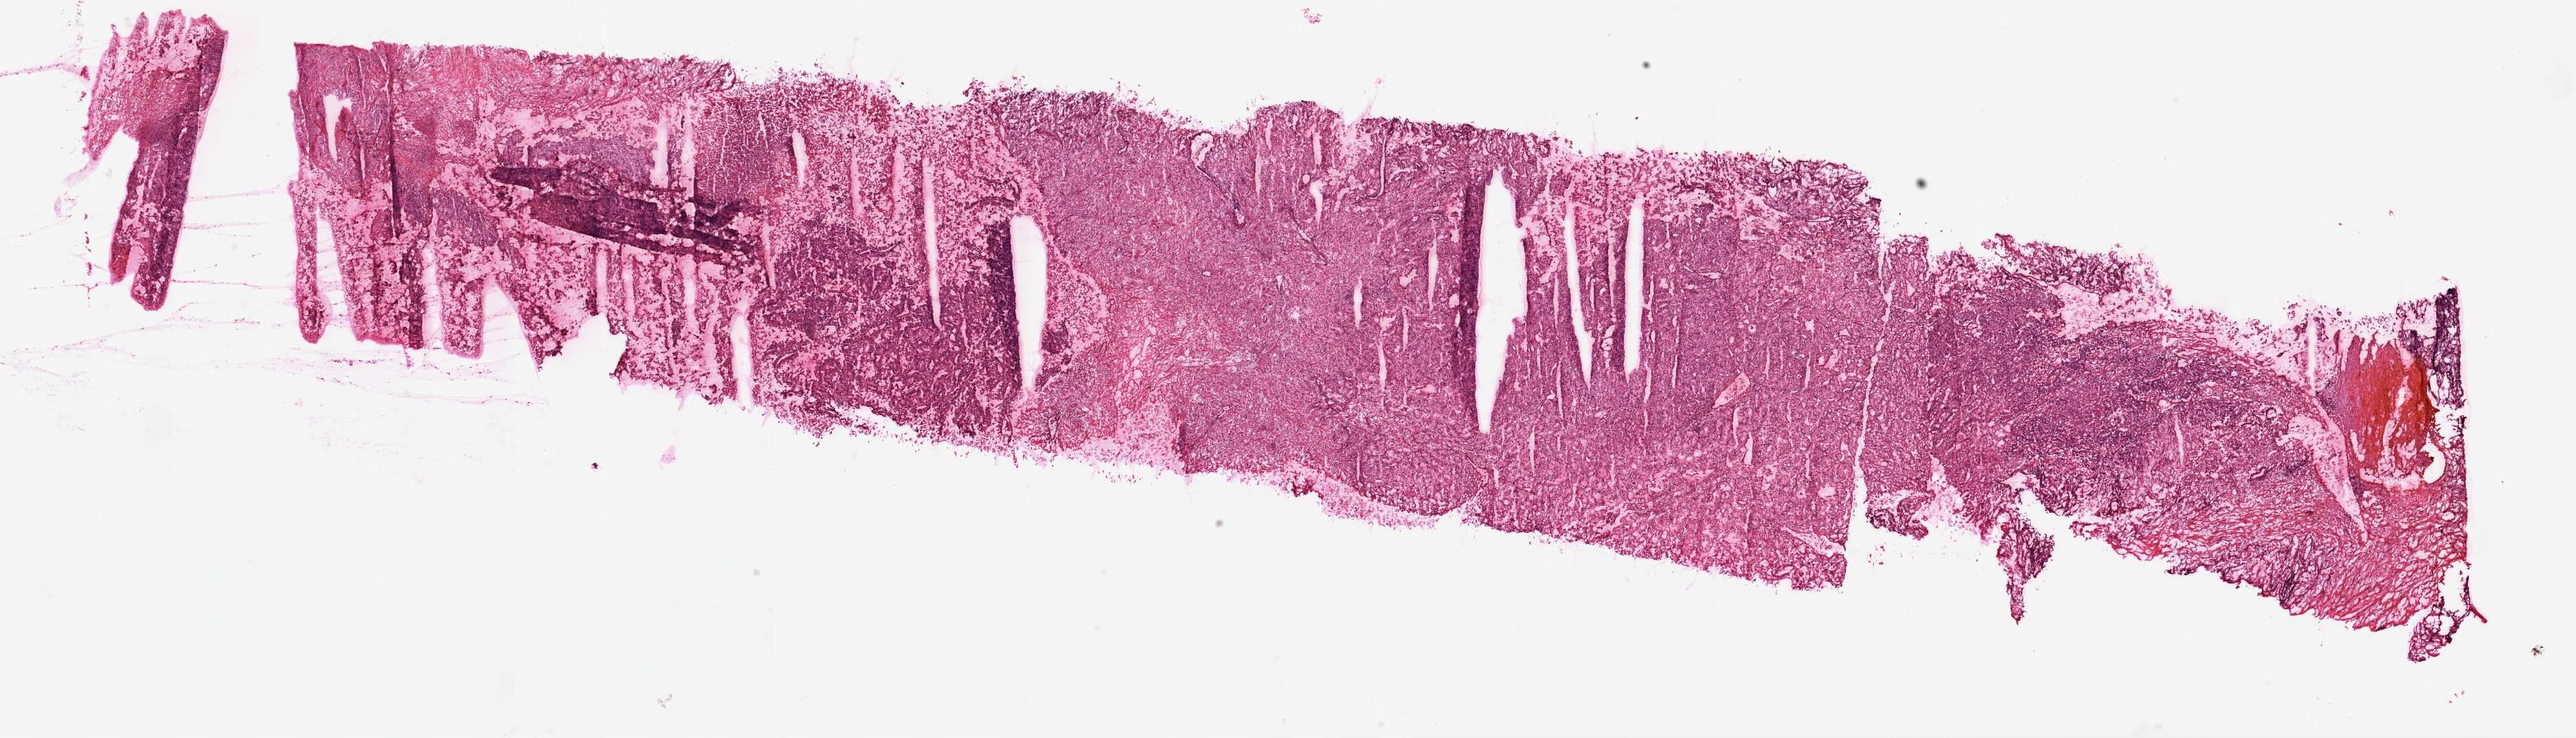
Whole-slide histology image, H&E-stained, a low-resolution overview of the entire scanned area, about 30.1 x 8.6 mm (slide scanned at 20x). Frozen section. Kidney, primary tumour sample. Patient: male, age at initial diagnosis 41 years. Histologic grade: G3 (poorly differentiated). Pathologist review of this section (percent, as recorded): tumour cells 90%, tumour nuclei 85%, normal cells 0%, stromal cells 10%, necrosis 0%.
TNM: T3a NX M0. Diagnosis: Clear cell adenocarcinoma, NOS. AJCC pathologic stage: III.